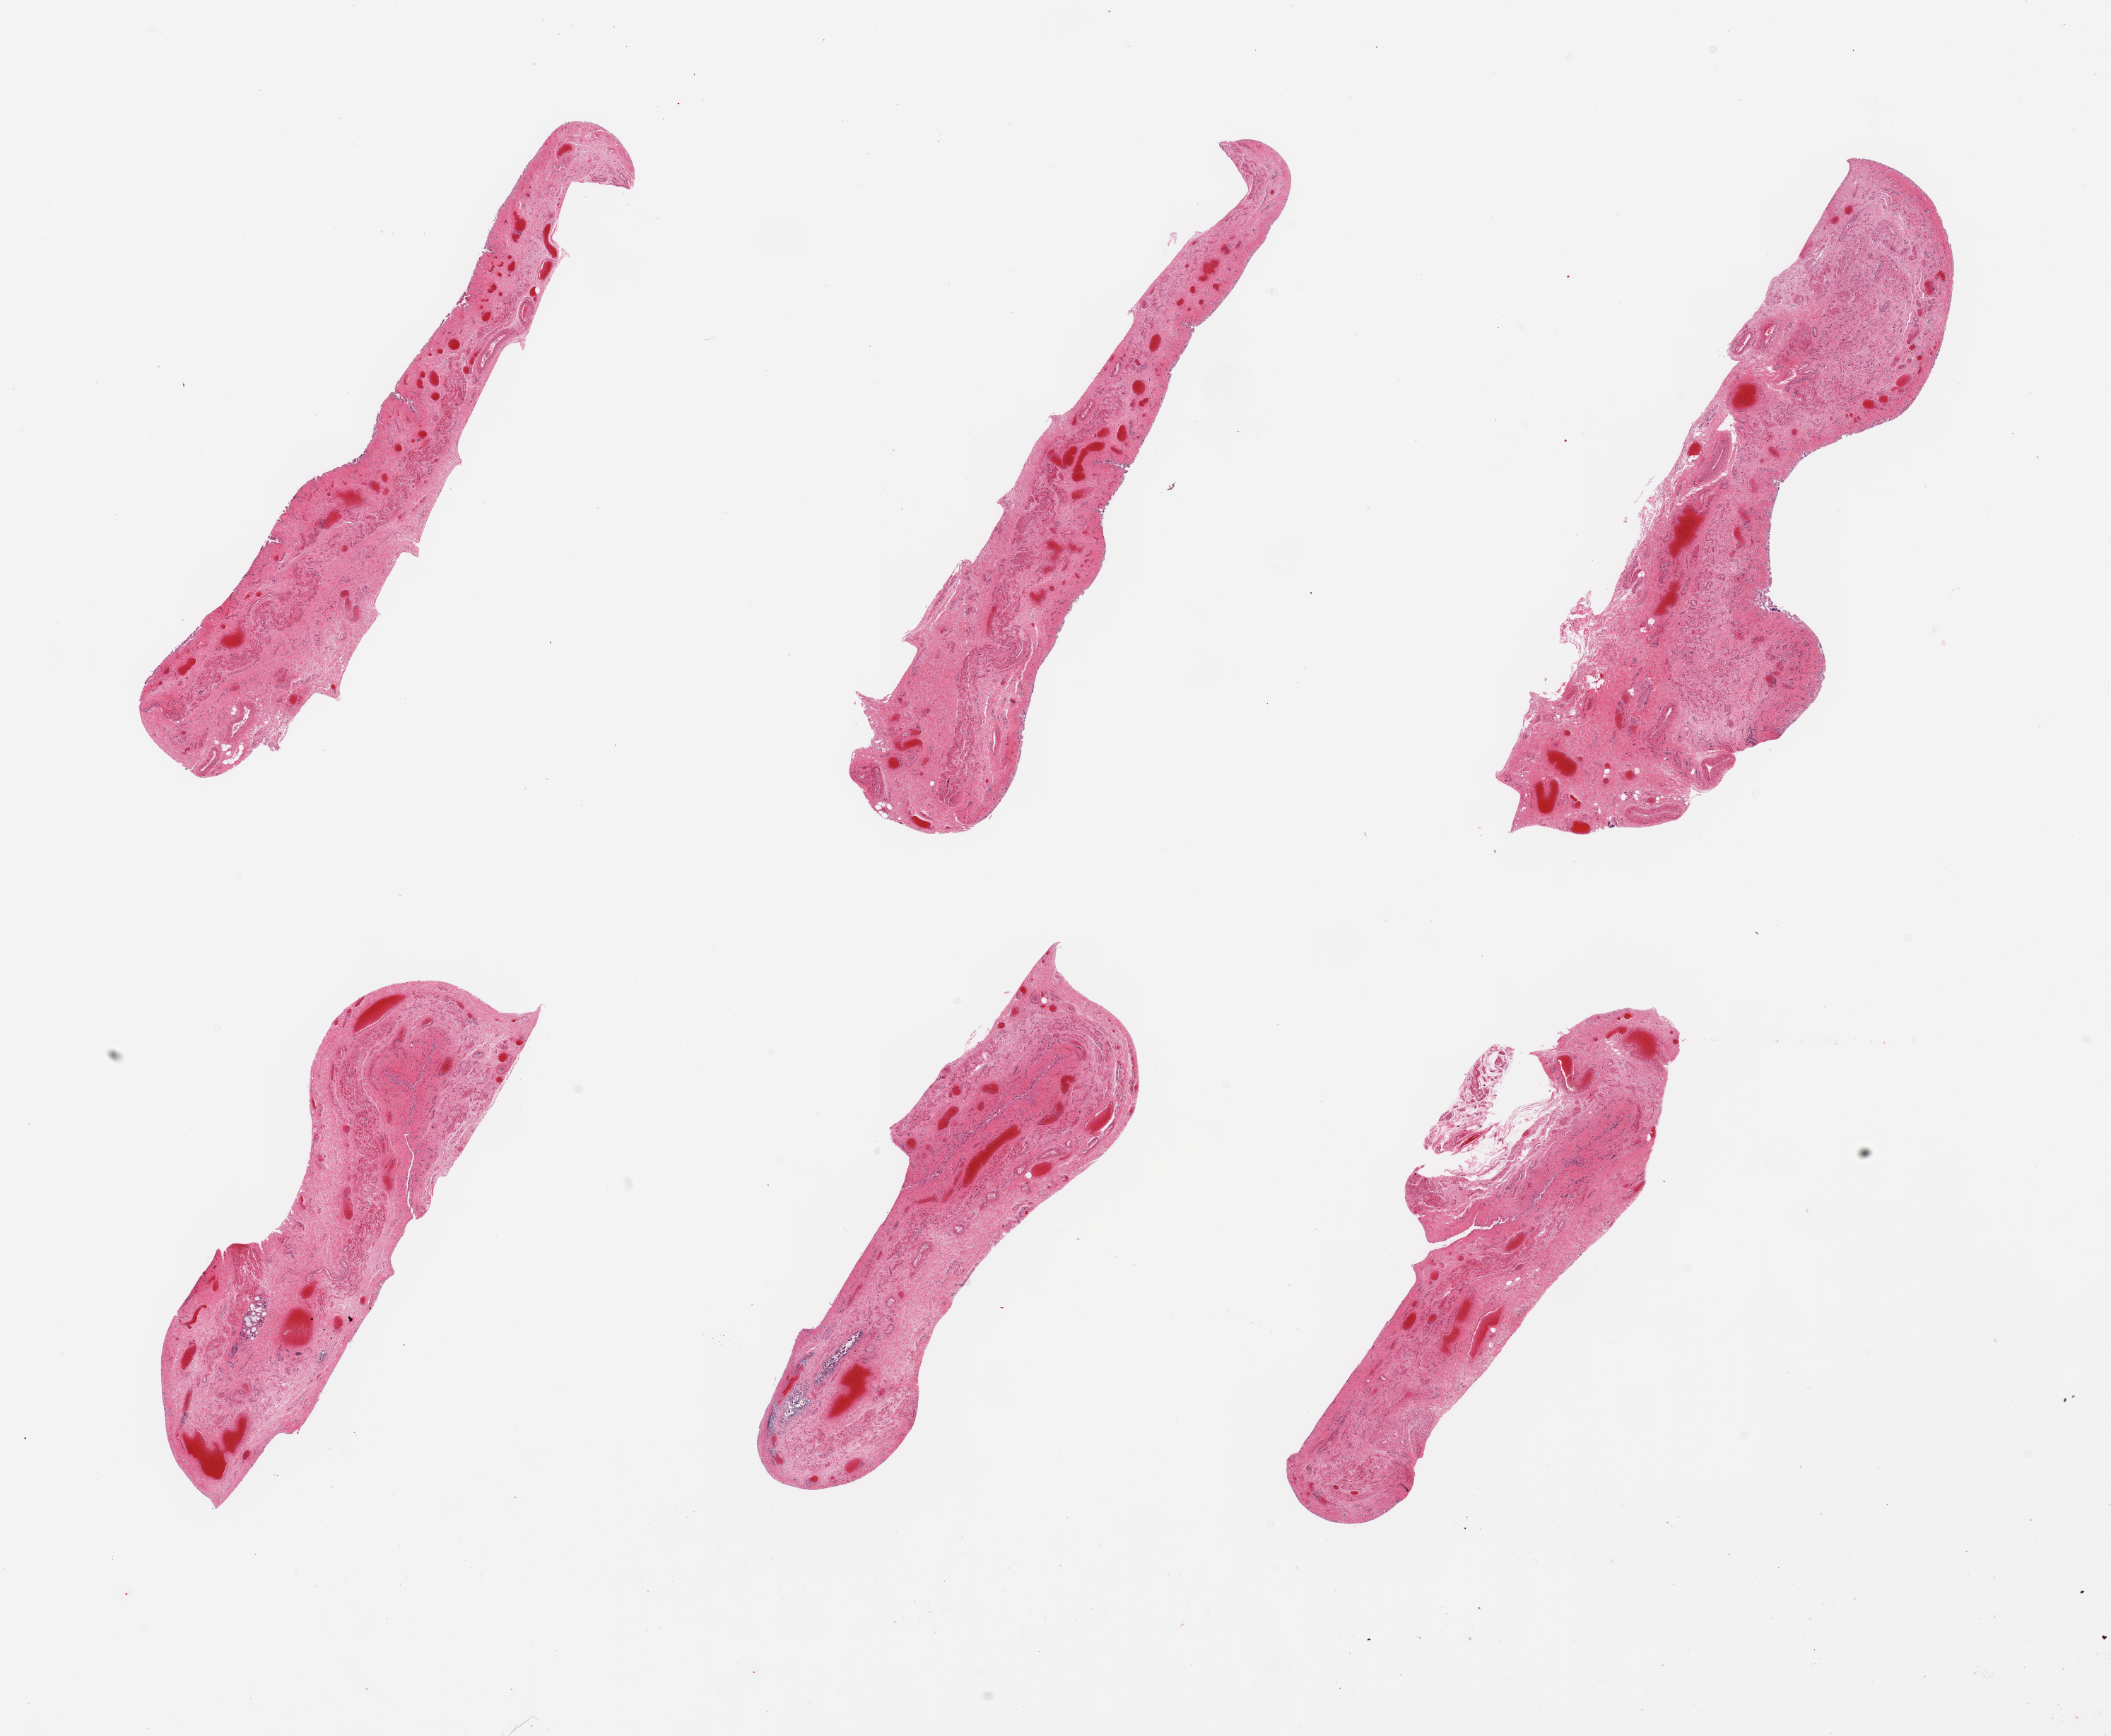
Whole-slide image, hematoxylin and eosin (H&E) stain, brightfield — a low-resolution overview of the entire scanned area, about 23.6 x 19.4 mm (acquisition: 20x scan), PAXgene-fixed paraffin-embedded (PFPE) section, section of esophageal mucous membrane (target tissue), donor tissue sample.
Review note (as recorded): 6 pieces, no residual target mucosa.